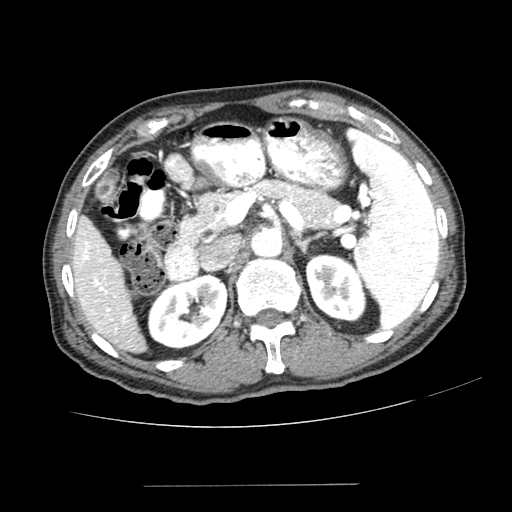
Contrast-enhanced abdominal CT (liver protocol), one axial slice; slice 144 of 187 in the series (ordered by position); reconstruction kernel SOFT; one of 2 acquisitions stored at this slice position; soft-tissue window (W 400 / L 40 HU); 512 × 512 image matrix, field of view 360 × 360 mm. Case-level facts recorded for this patient, not image findings: diagnosis: hepatocellular carcinoma (patient treated with transarterial chemoembolisation; whether this scan precedes or follows treatment is not stated here); TNM stage (as recorded): Stage-I; Child-Pugh class: A; tumour differentiation: poorly differentiated.
Structures marked on this image (semi-automatically segmented with operator editing):
- liver parenchyma outside the tumour (the mass and vessels are separate outlines, so this box may not span the whole liver): box from (x=70, y=215) to (x=146, y=352) px
- liver vessels: (x=80, y=241)–(x=128, y=331)